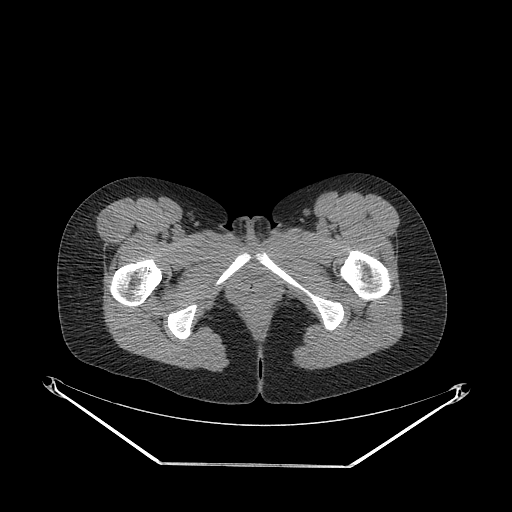
CT of an extremity soft-tissue mass (from a PET/CT study), one axial slice. Slice 53 of 267 in the series (ordered by position). Reconstruction kernel STANDARD. Soft-tissue window (W 400 / L 40 HU). 3.75 mm slice thickness. 512 × 512 image matrix. Female patient. From the clinical record (not read from this slice): histological type: synovial sarcoma; grade: intermediate; site of the primary tumour: right thigh.
Annotated regions visible in this slice (expert contour drawn on MRI and transferred to this co-registered scan by the dataset authors):
- gross tumour volume including surrounding oedema: box from (x=93, y=217) to (x=115, y=245) px
- gross tumour volume (mass): (x=93, y=217)–(x=115, y=245)